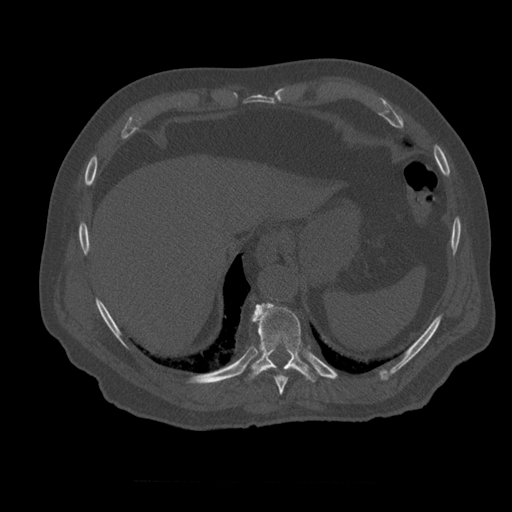
CT including the spine, one axial slice. Slice 306 of 399 in the series (ordered by position). Reconstruction kernel STANDARD. 120 kVp. Bone window (W 1800 / L 400 HU). 512 × 512 image matrix, field of view 407 × 407 mm. Patient age 73 years. From the clinical record (not read from this slice): primary cancer: prostate; vertebrae with lytic lesions (as recorded): L2.
Outlined on this slice (semi-automatic segmentation, software-assisted and operator-edited):
- T10 vertebra: bounding box (x1, y1, x2, y2) in pixels: (245, 303, 320, 383)
- T9 vertebra: (268, 368, 288, 395)